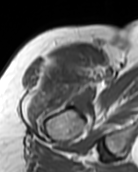
MRI of an extremity soft-tissue mass, one axial slice. Slice 81 of 99 in the series (ordered by position). MR volume resampled by the dataset authors to the PET/CT grid (not the native acquisition matrix). 3.27 mm slice thickness. 138 × 172 image matrix, field of view 135 × 168 mm. Female patient. From the clinical record (not read from this slice): histological type: pleiomorphic undifferentiated sarcoma; grade: high; site of the primary tumour: right quadricep.
Annotated regions visible in this slice (expert contour drawn on MRI and transferred to this co-registered scan by the dataset authors):
- gross tumour volume including surrounding oedema: box from (x=26, y=54) to (x=93, y=124) px
- gross tumour volume (mass): (x=41, y=54)–(x=93, y=99)